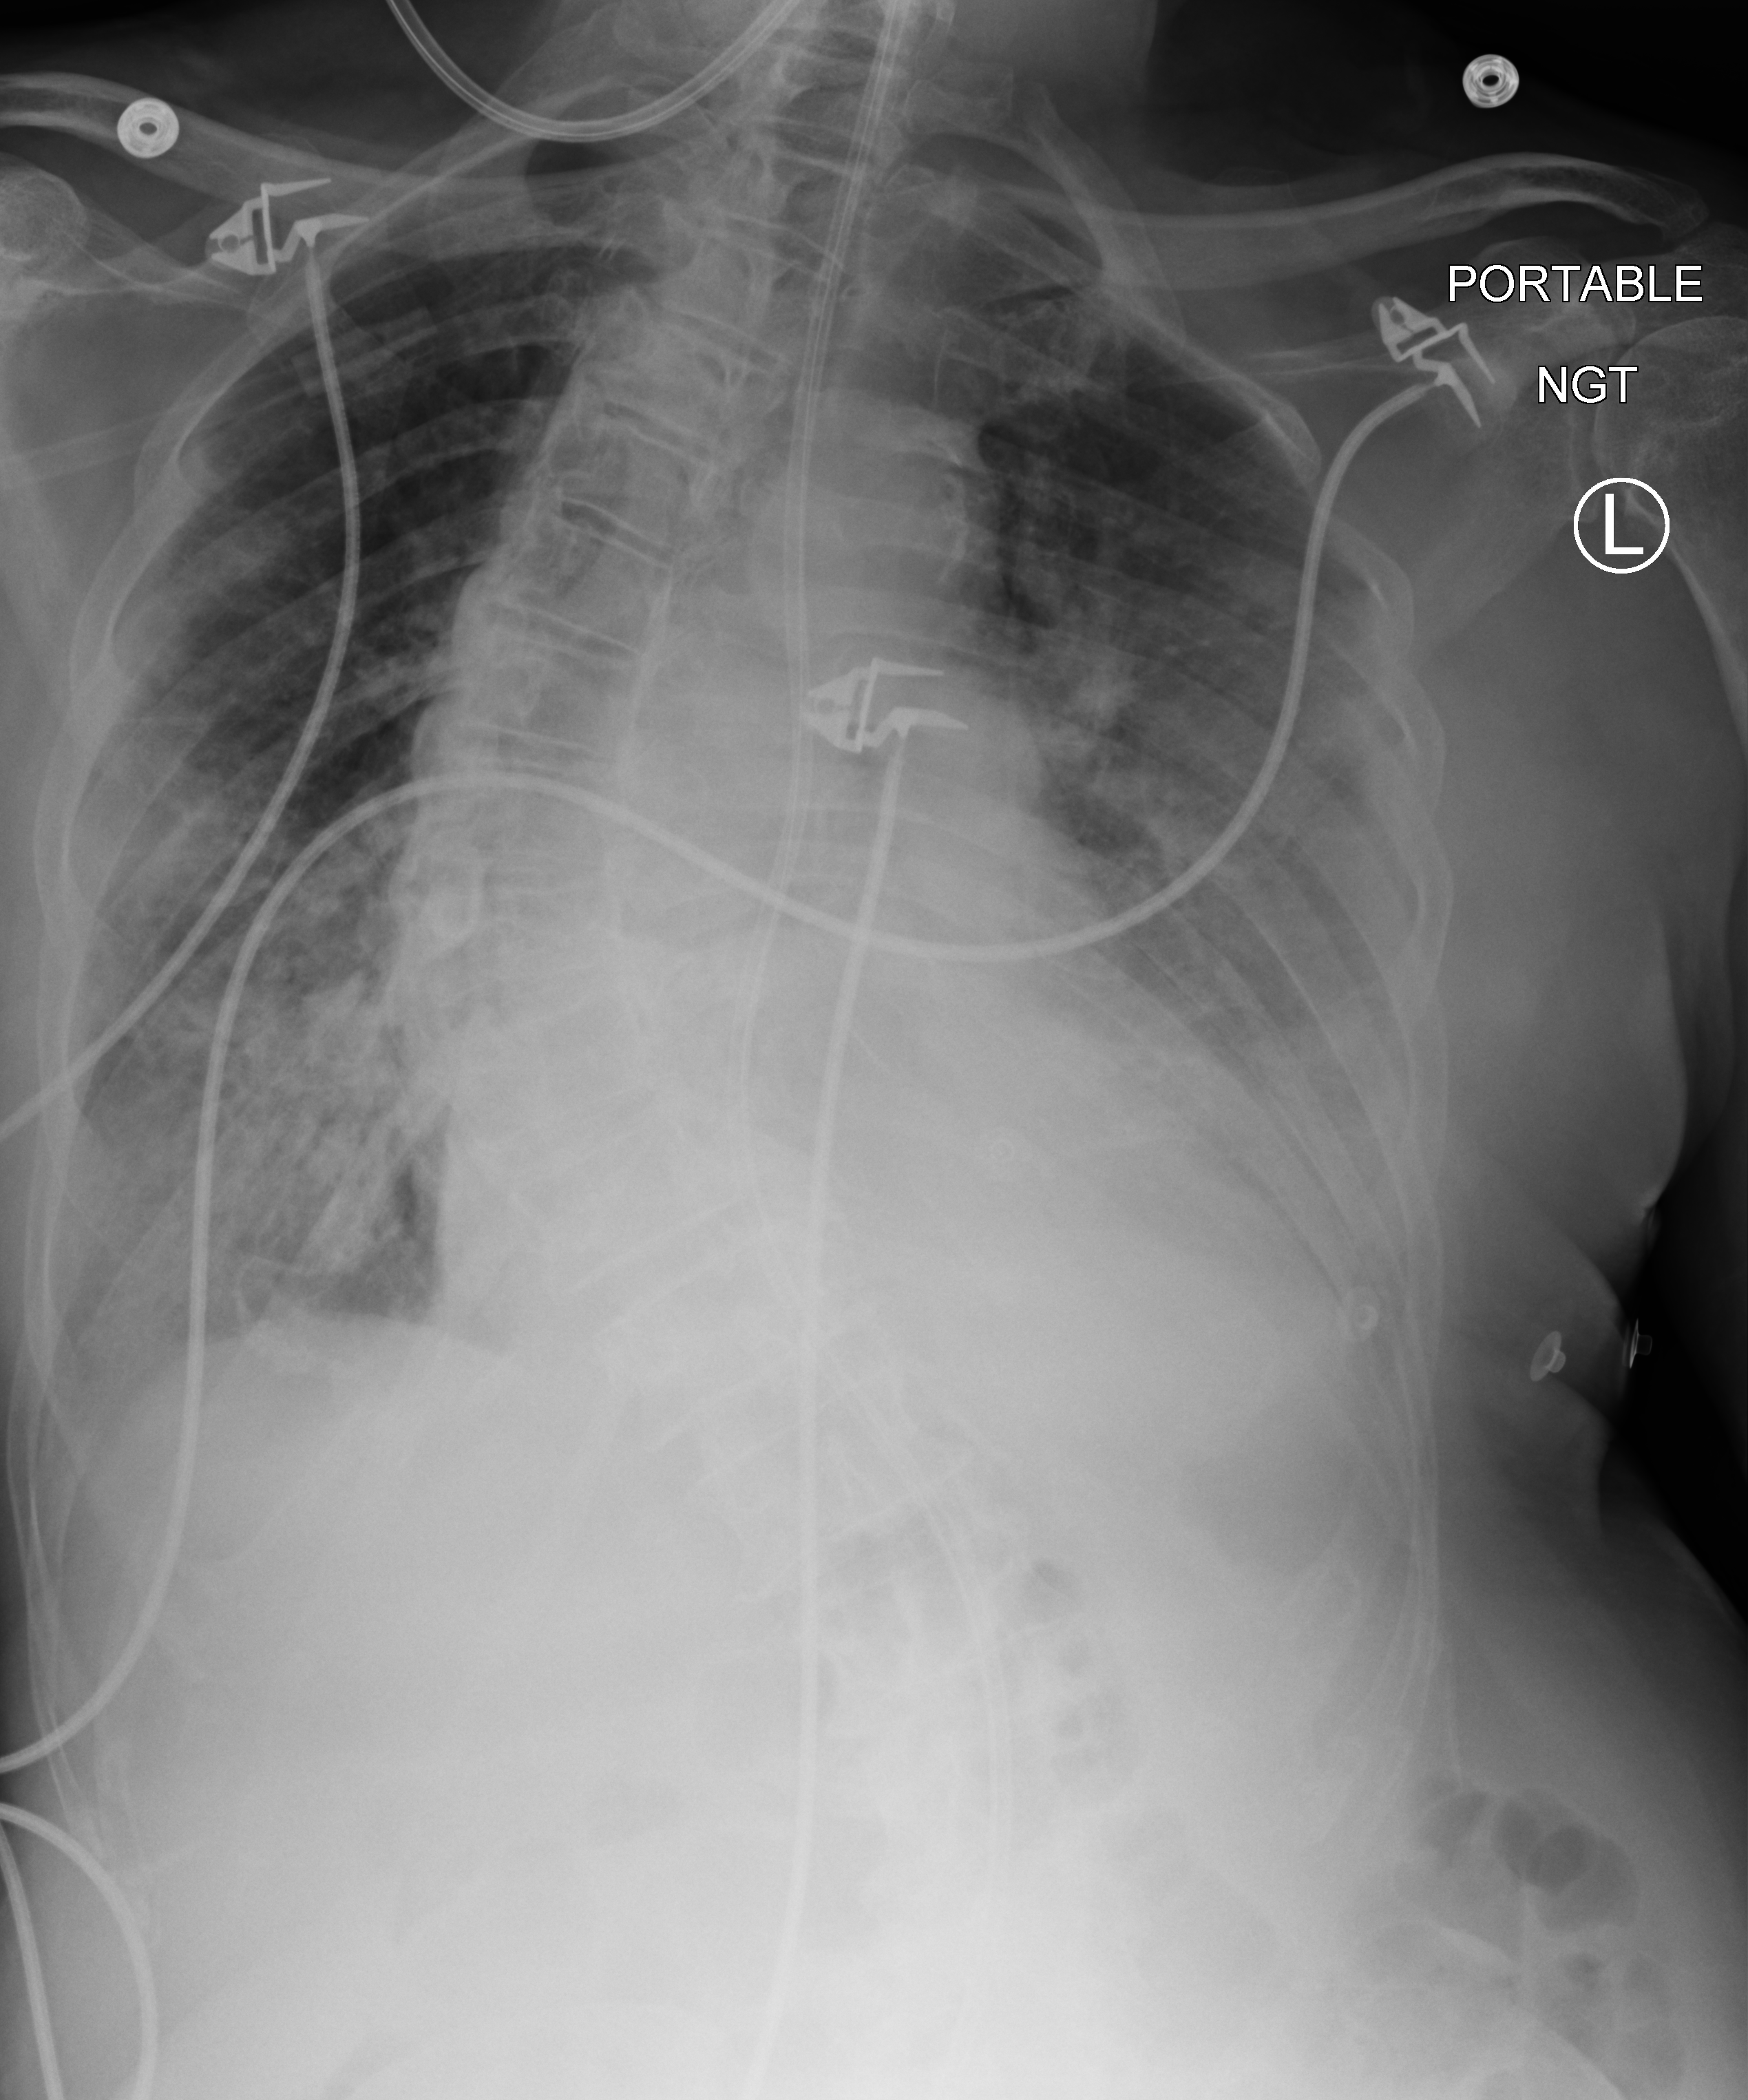
Bedside chest radiograph (computed radiography), anteroposterior (AP) projection. Male patient hospitalised with COVID-19, age 75–90 years.
Admission-level facts for this patient (not findings on this image; timing relative to this image not recorded):
- admitted to intensive care during this hospital stay: no
- mechanically ventilated during this hospital stay: no